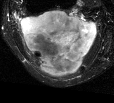
MRI of an extremity soft-tissue mass, one axial slice; slice 25 of 44 in the series (ordered by position); T2-weighted fat-saturated; MR volume resampled by the dataset authors to the PET/CT grid (not the native acquisition matrix); 114 × 103 image matrix, field of view 111 × 101 mm. Female patient. Case-level facts recorded for this patient, not image findings: histological type: liposarcoma; site of the primary tumour: right thigh.
Structures marked on this image (expert contour drawn on MRI and transferred to this co-registered scan by the dataset authors):
- gross tumour volume (mass): bounding box (x1, y1, x2, y2) in pixels: (20, 9, 98, 76)